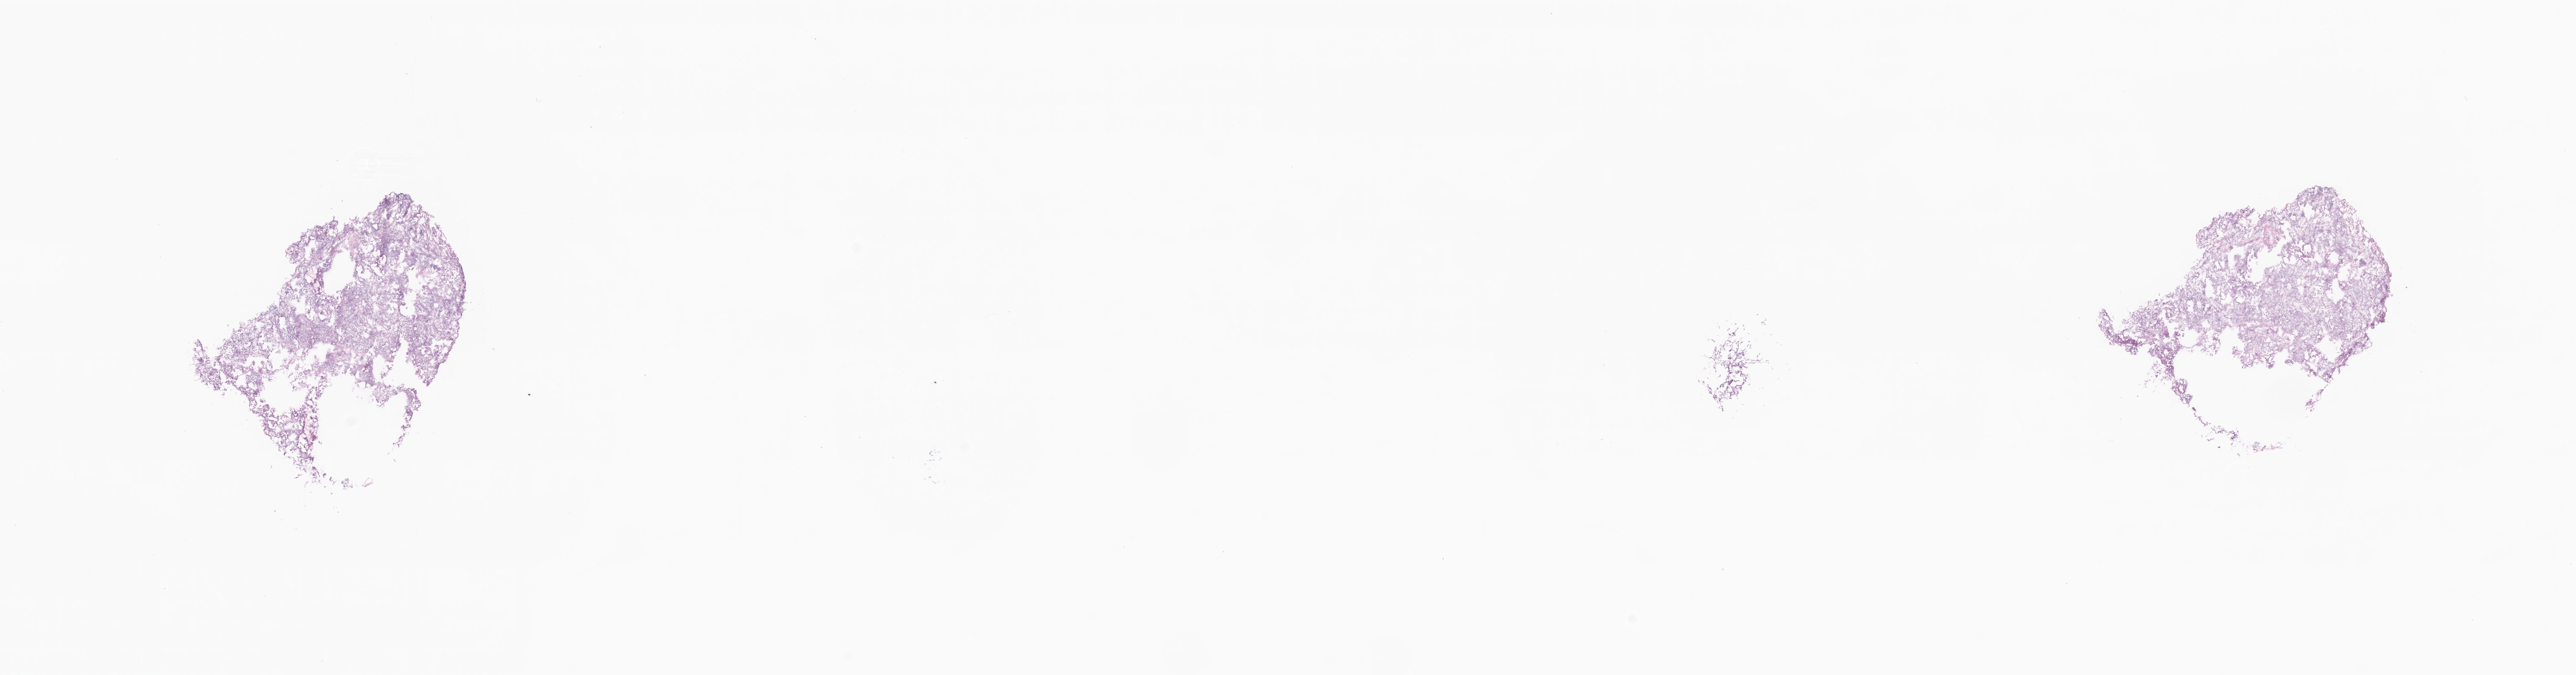
Whole-slide image, H&E stain — whole scanned area (about 25.4 x 6.7 mm) shown as a low-resolution overview; frozen section (tissue freezing medium); specimen: primary tumor; anatomic site: breast (left). Patient: female, age at initial diagnosis 73 years. Pathologist review of this section (percent, as recorded): tumor cells 80%, tumor nuclei 90%, stromal cells 10%, necrosis 10%, normal cells 0%. Inflammatory infiltration, as recorded: lymphocyte infiltration 0%, monocyte infiltration 0%, neutrophil infiltration 0%.
Diagnosis: Metaplastic carcinoma, NOS.